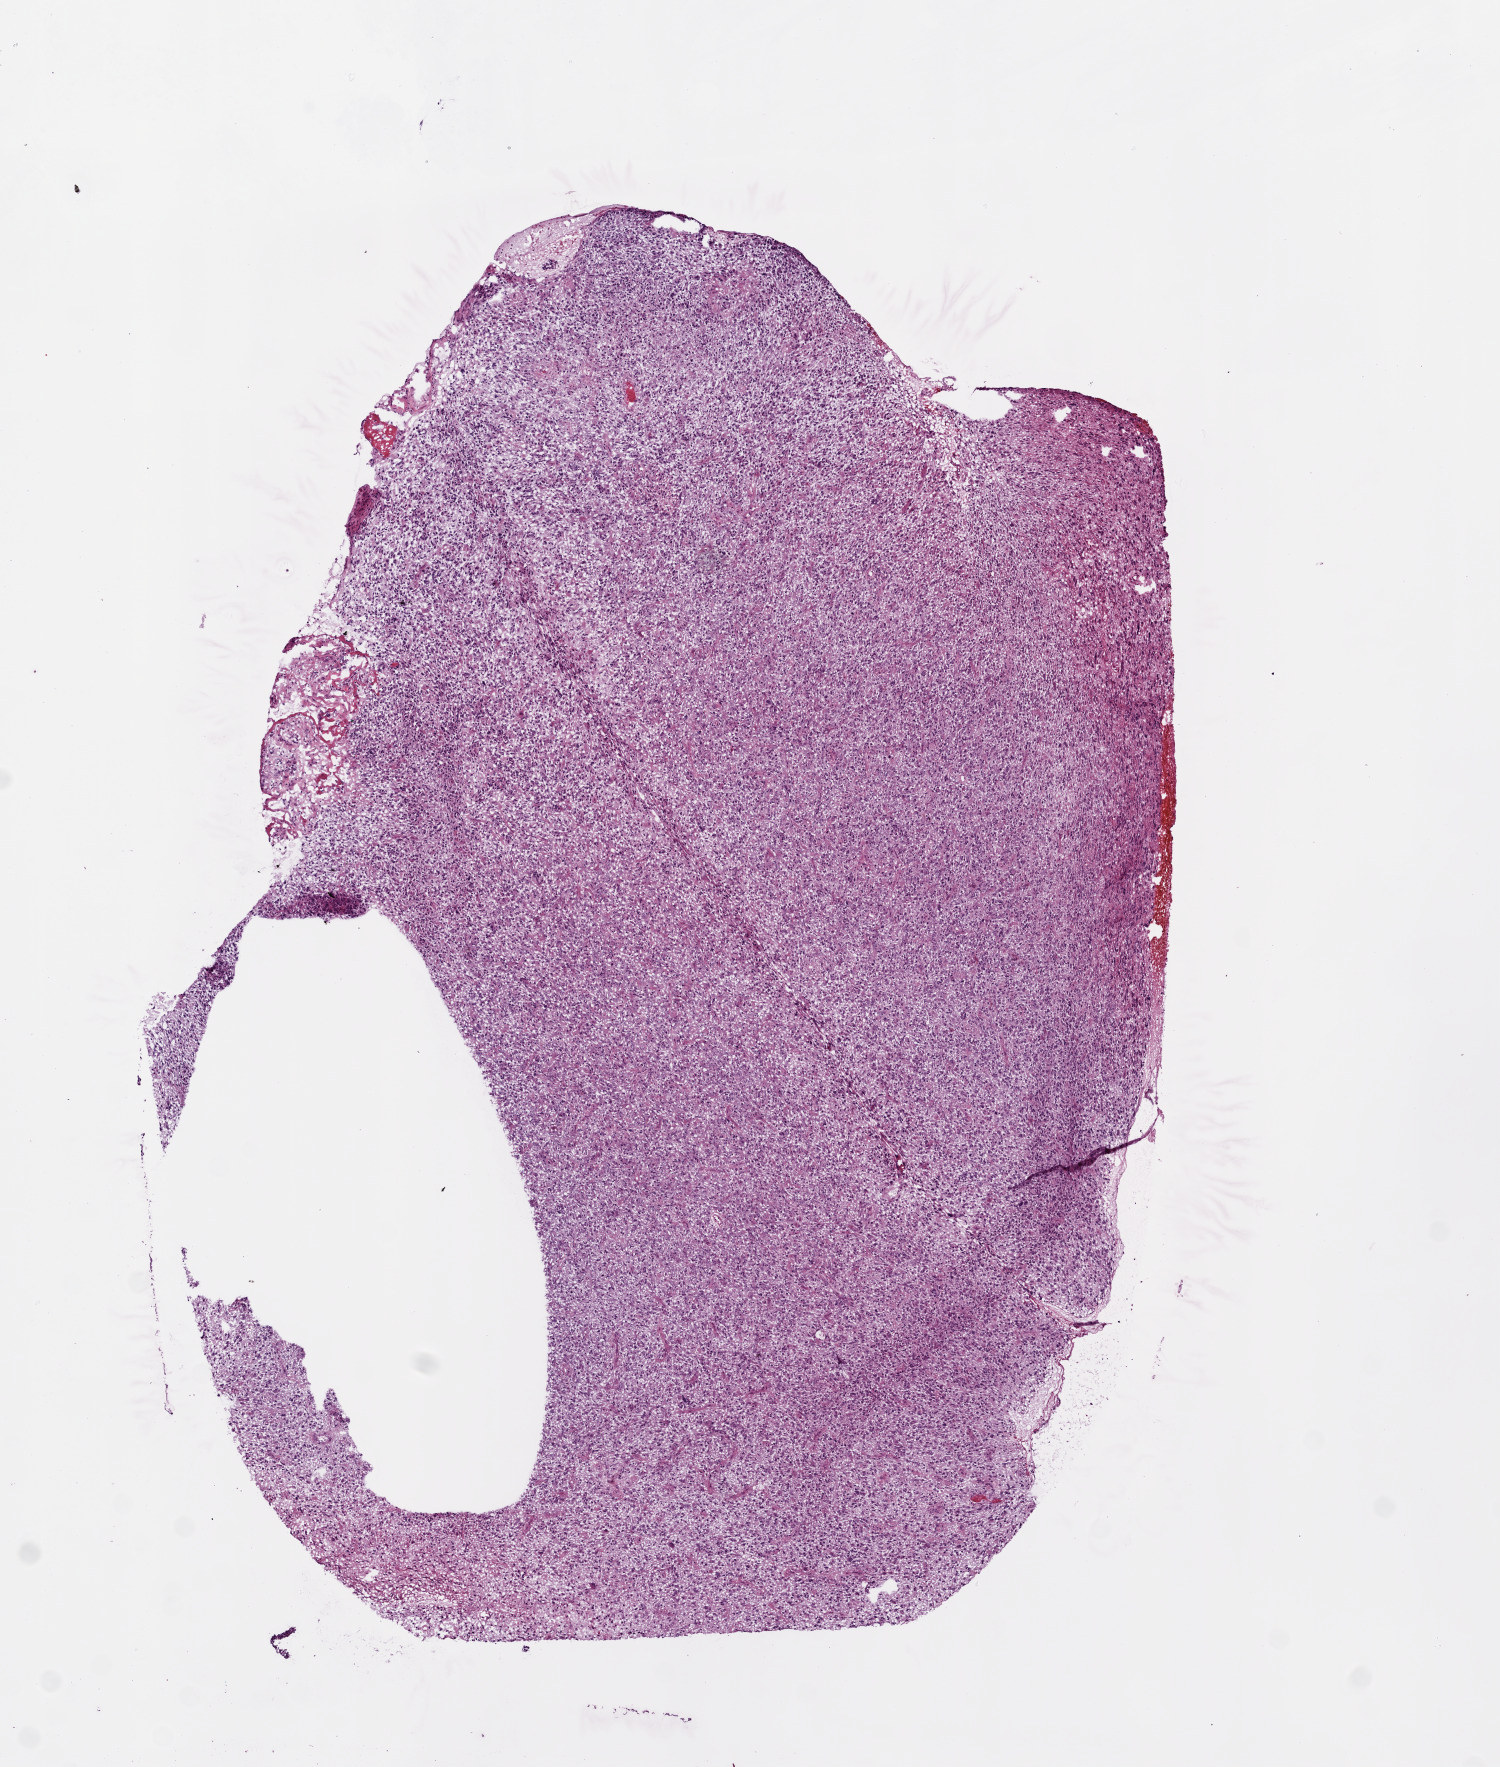
H&E whole-slide image, shown as a low-resolution overview of the whole scanned area (about 6.0 x 7.1 mm, acquisition: 20x scan); frozen section; brain, primary tumour sample. Patient: female, age at initial diagnosis 66 years. Pathologist review of this section (percent, as recorded): tumour cells 100%, tumour nuclei 80%, normal cells 0%, stromal cells 0%, necrosis 0%.
* histologic diagnosis: Glioblastoma